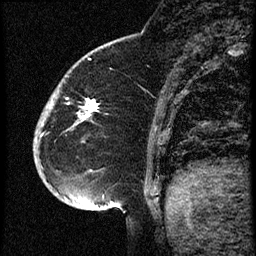
Breast MRI (dynamic contrast-enhanced), one sagittal slice. Position 15 of 60 along the scan axis. Dynamic contrast-enhanced study with each time point stored as its own series, time point 2 of 3 at this slice position (early post-contrast, ordered by acquisition time). 1.5 T. TE 4.2 ms, TR 18.9 ms. 2 mm slice thickness. 256 × 256 image matrix, field of view 200 × 200 mm. Female patient. Case-level facts recorded for this patient, not image findings: setting: breast cancer imaged before/during neoadjuvant chemotherapy; receptor status: HR-positive, HER2-negative.
Outlined on this slice (semi-automatic segmentation, software-assisted and operator-edited):
- analysis volume of interest (the breast-tissue region the enhancement analysis was run in; not a lesion): bounding box [x1, y1, x2, y2] px = [34, 87, 102, 173]
- tumour enhancement mask (voxels above the 100 % enhancement threshold inside the analysis volume of interest): [87, 103, 98, 114]